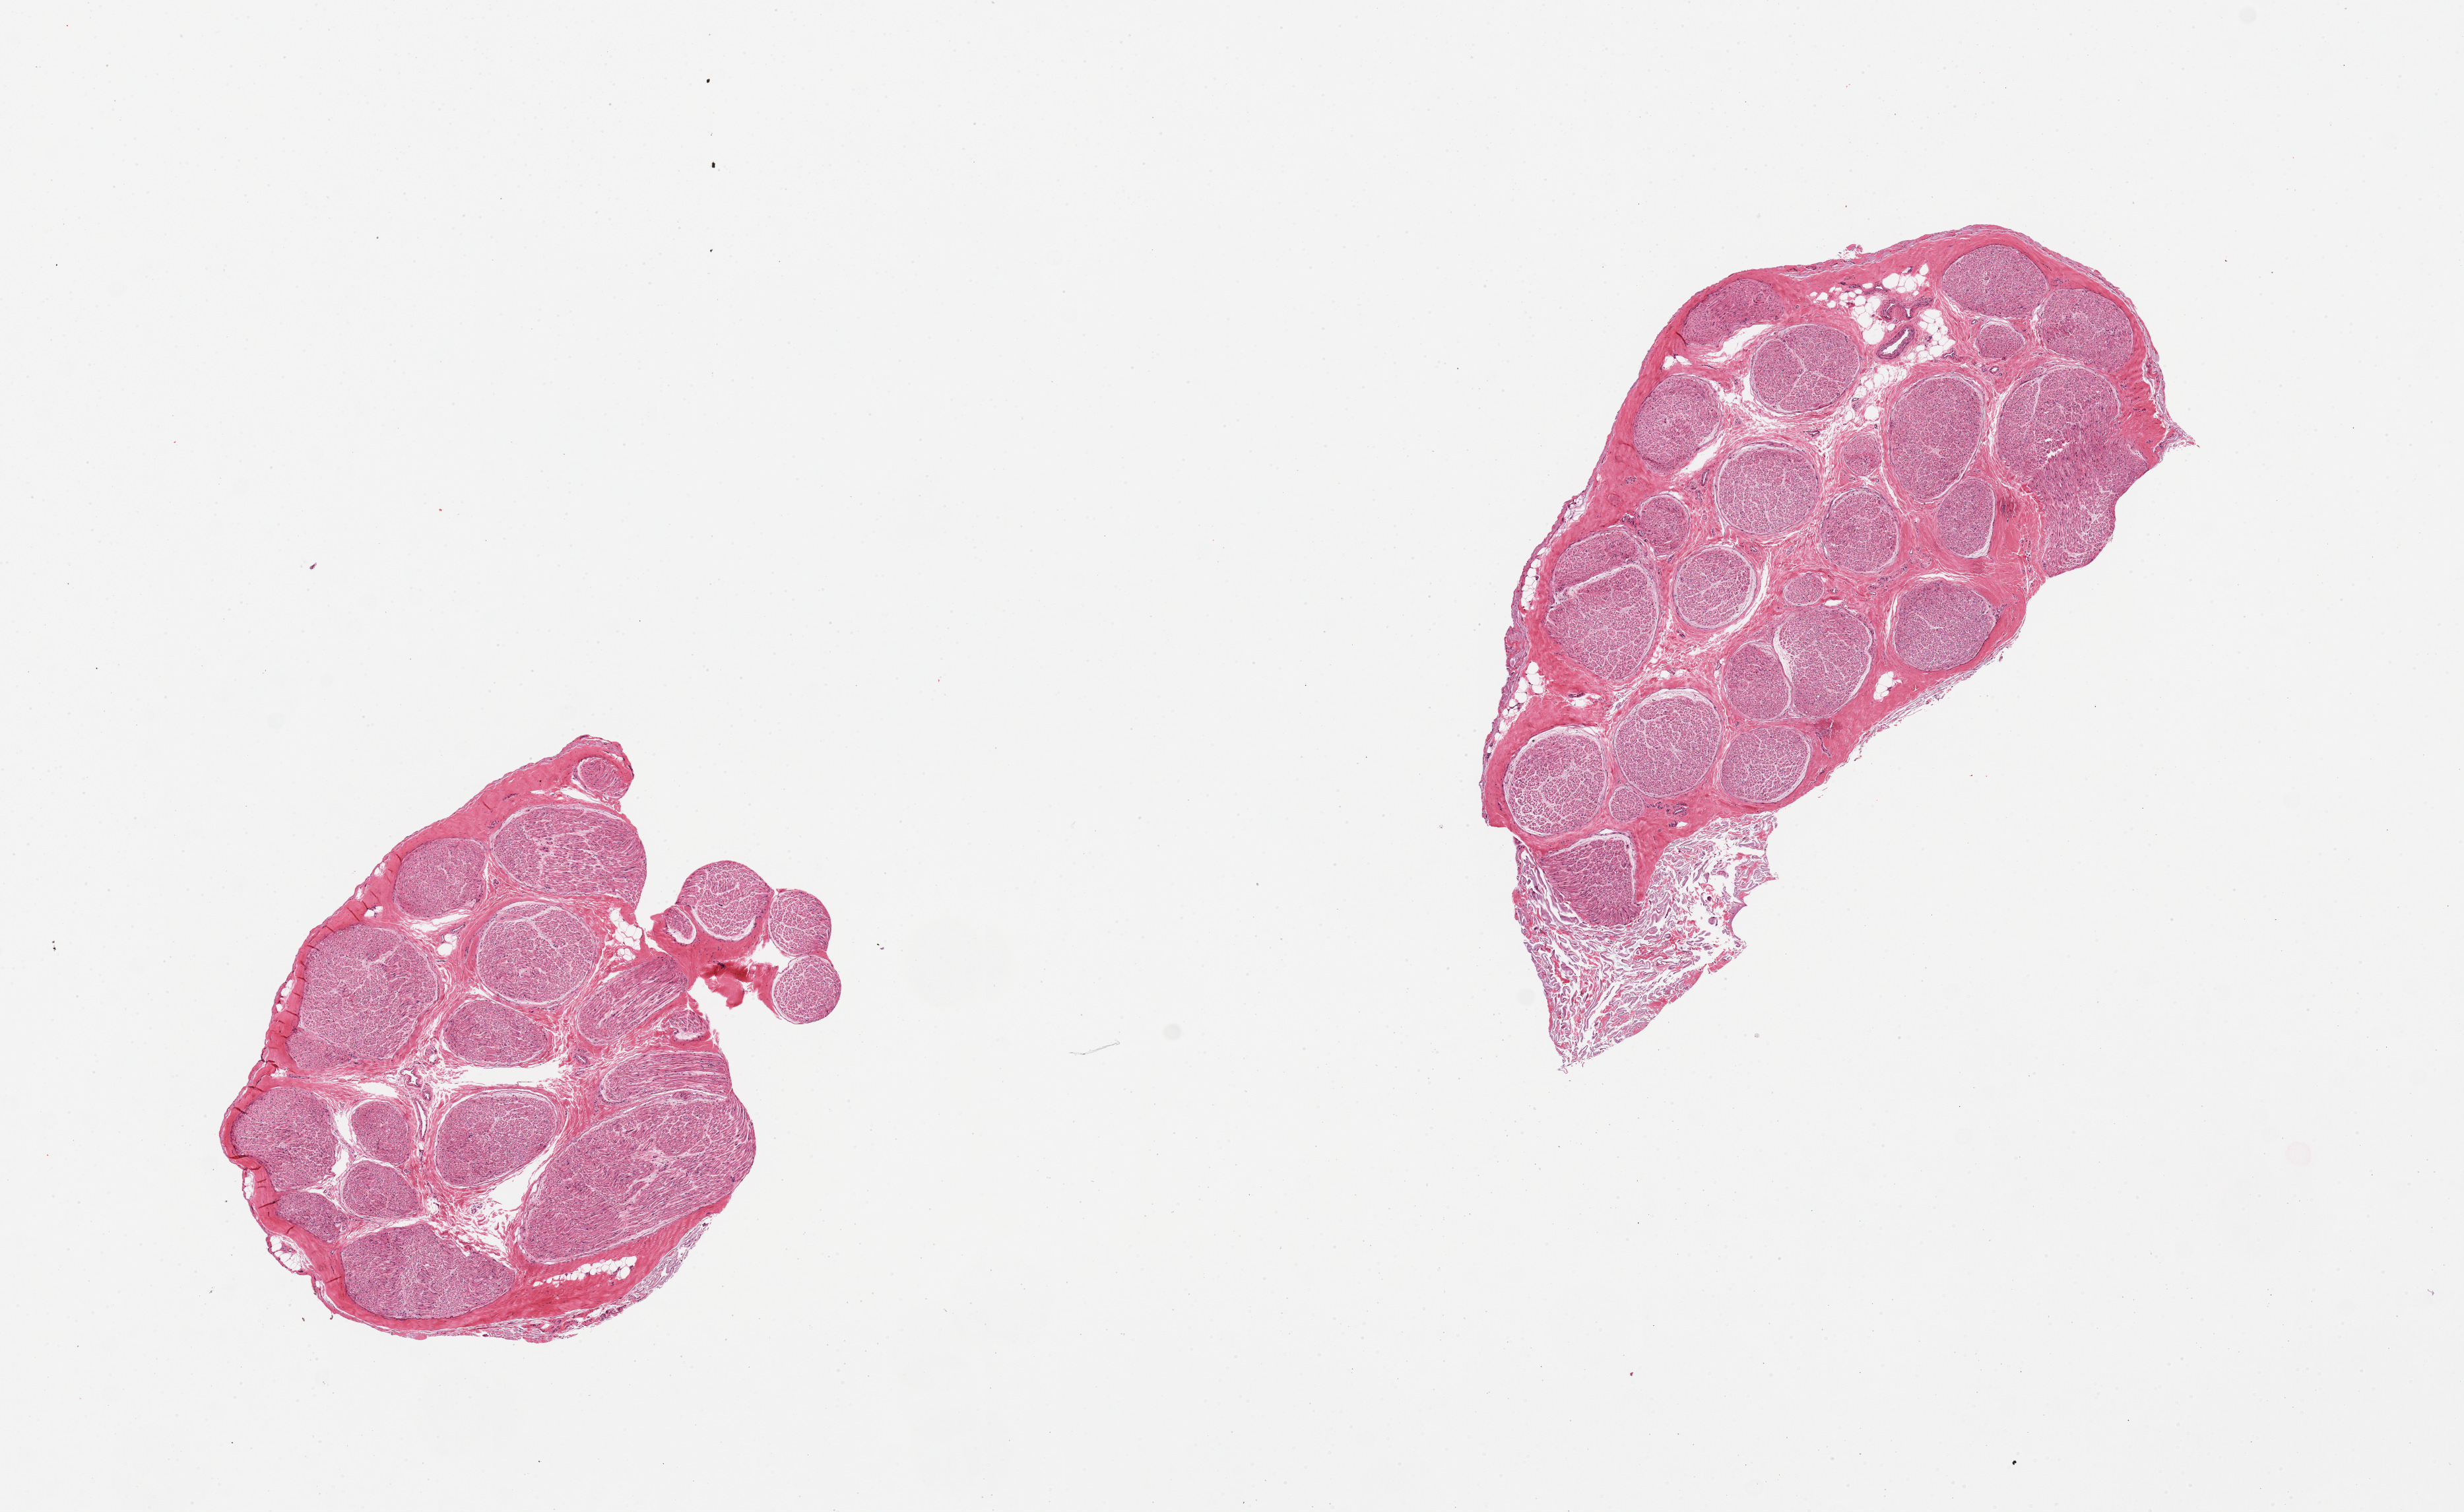
Whole-slide image, hematoxylin and eosin (H&E) stain, a low-resolution overview of the entire scanned area, about 14.8 x 9.1 mm (slide scanned at 20x), PAXgene-fixed, paraffin-embedded tissue, sampled site (target tissue): tibial nerve, donor tissue sample. Donor: male.
Pathologist's review note for this sample: 2 pieces; no fat.